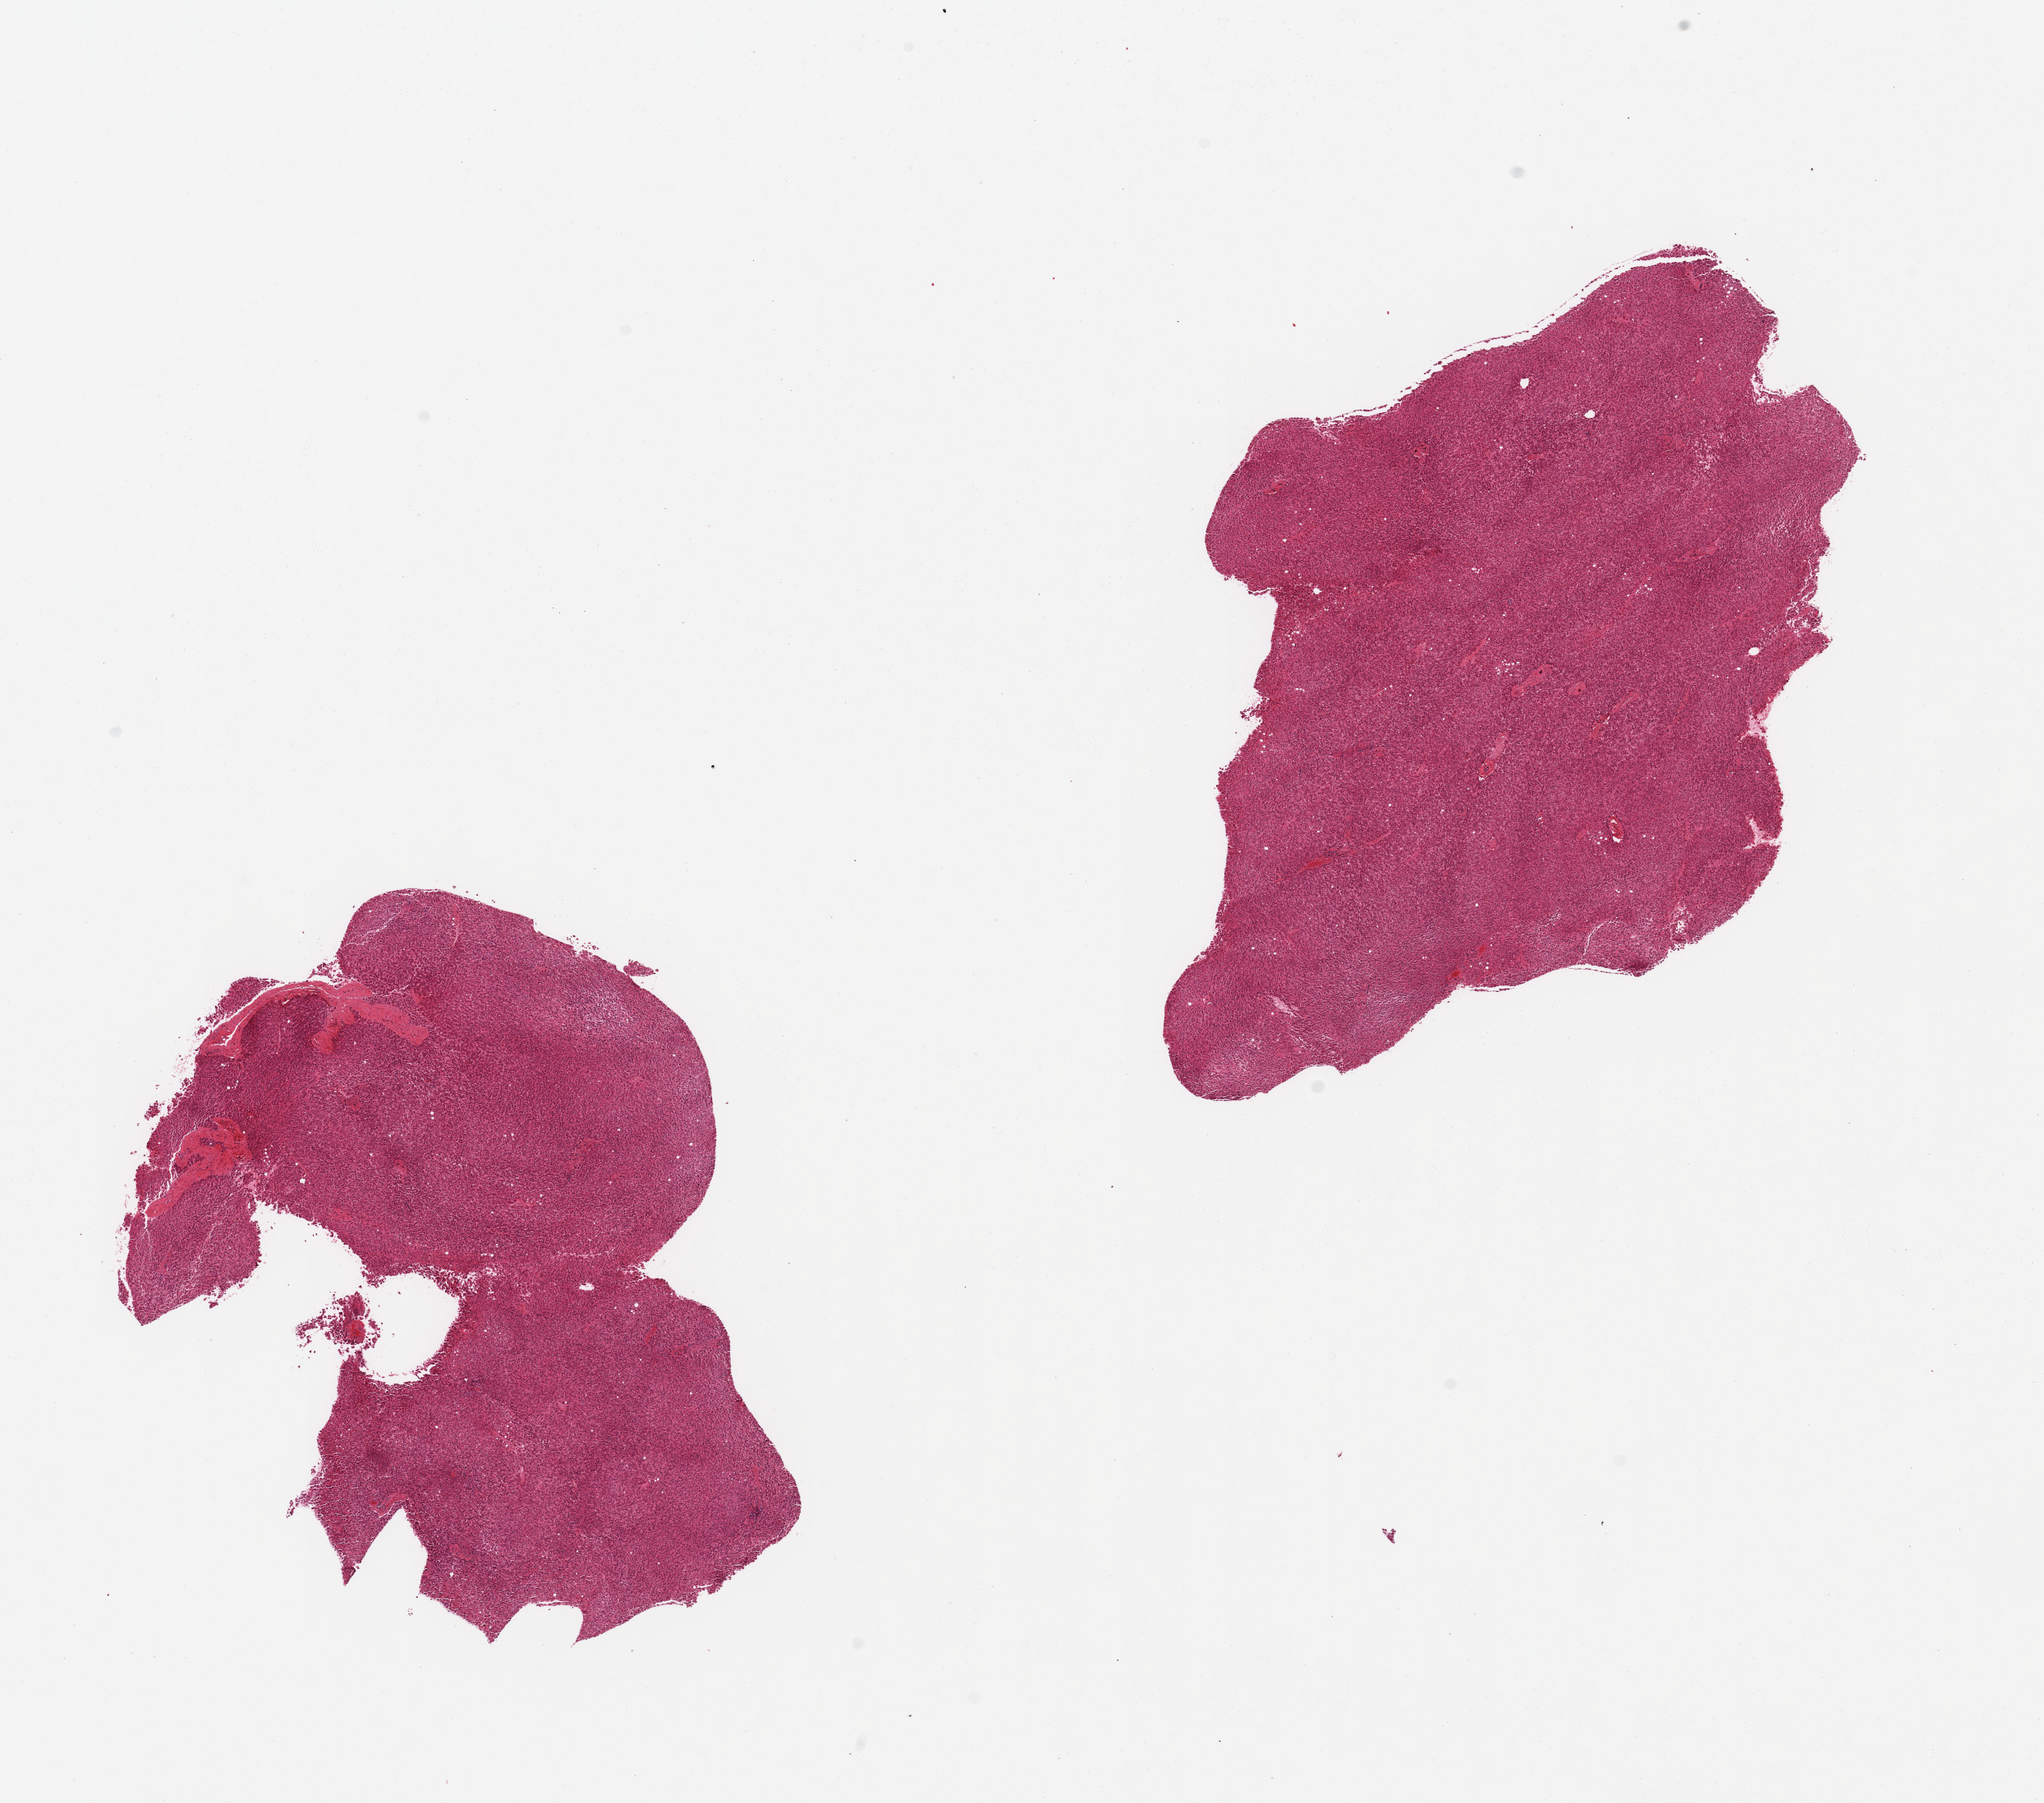
Haematoxylin and eosin whole-slide image, a low-resolution overview of the entire scanned area, about 19.7 x 17.4 mm (acquisition: 20x scan), PAXgene-fixed, paraffin-embedded tissue, target tissue: liver, tissue donor sample. Donor: female.
Pathologist's review note for this sample: 2 pieces.